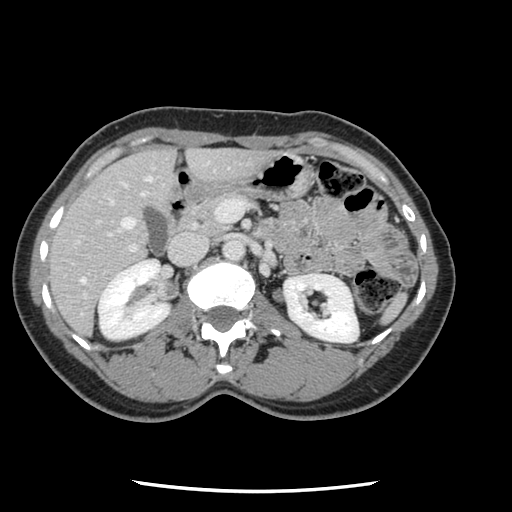
Contrast-enhanced abdominal CT, one axial slice. Slice 52 of 134 in the series (ordered by position). 120 kVp. Intravenous contrast given. Soft-tissue window (W 400 / L 40 HU). 512 × 512 image matrix, field of view 330 × 330 mm. Female patient, age 43 years. Case-level facts recorded for this patient, not image findings: diagnosis: colorectal cancer liver metastases, imaged before liver resection; multiple liver metastases: yes; largest metastasis: 3.4 cm.
Structures marked on this image (outlined manually by an expert reader):
- hepatic veins: bounding box [x1, y1, x2, y2] px = [80, 176, 153, 284]
- liver: [50, 148, 265, 335]
- planned liver remnant (the part of the liver to remain after resection): [50, 148, 175, 331]
- portal vein (with intrahepatic branches): [72, 201, 247, 299]